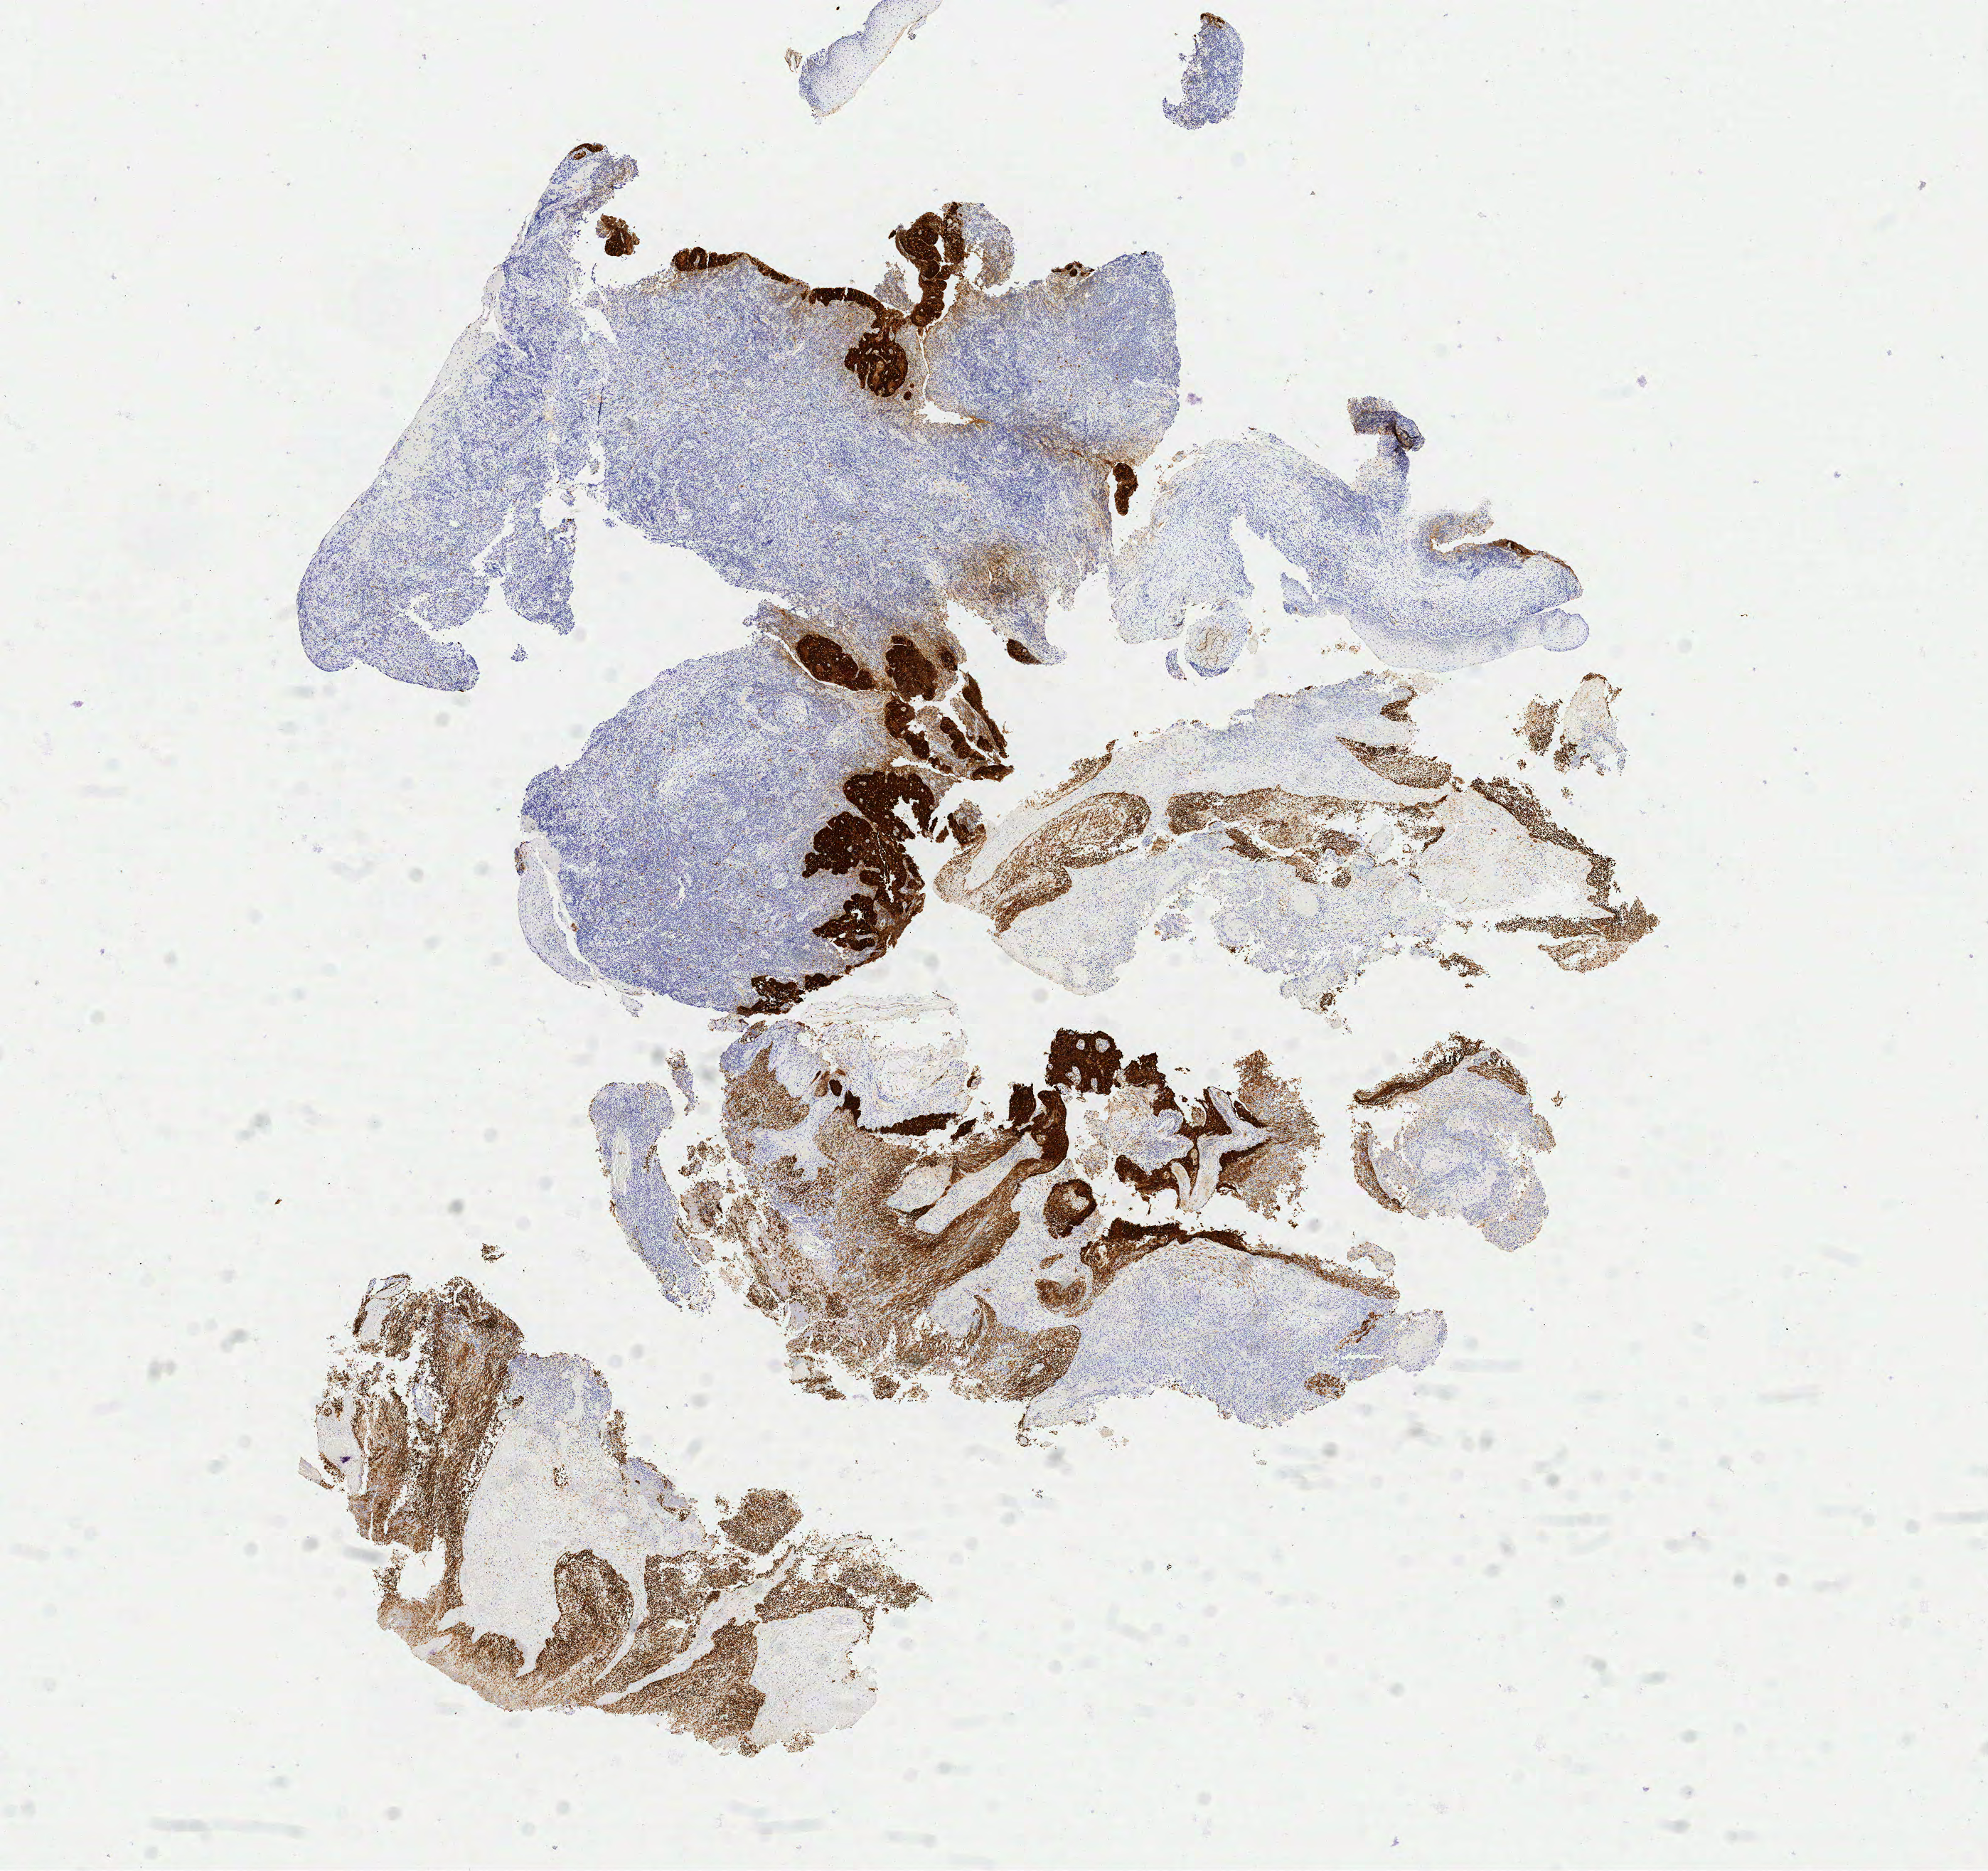
Whole-slide image, immunohistochemical stain for p16 (p16INK4a), shown as a low-resolution overview of the whole scanned area (about 11.1 x 10.5 mm). Tumor tissue. Anatomic site: cervix. Patient: female, 61 years old.
Histologic diagnosis: Squamous cell carcinoma, large cell, nonkeratinizing, NOS.